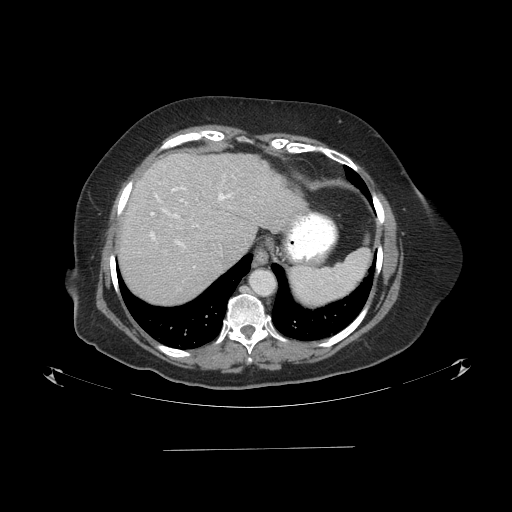
Contrast-enhanced abdominal CT (liver protocol), one axial slice; position 72 of 103 along the scan axis; reconstruction kernel STANDARD; 120 kVp; one of 2 acquisitions stored at this slice position; soft-tissue window (W 400 / L 40 HU); 2.5 mm slice thickness; 512 × 512 image matrix, field of view 500 × 500 mm. Case-level facts recorded for this patient, not image findings: diagnosis: hepatocellular carcinoma (patient treated with transarterial chemoembolisation; whether this scan precedes or follows treatment is not stated here); TNM stage (as recorded): Stage-IIIA; Child-Pugh class: A; tumour differentiation: poorly differentiated; tumour nodularity: multinodular.
Annotated regions visible in this slice (semi-automatically segmented with operator editing):
- liver parenchyma outside the tumour (the mass and vessels are separate outlines, so this box may not span the whole liver): bounding box (x1, y1, x2, y2) in pixels: (118, 152, 306, 304)
- liver vessels: (150, 187, 231, 246)